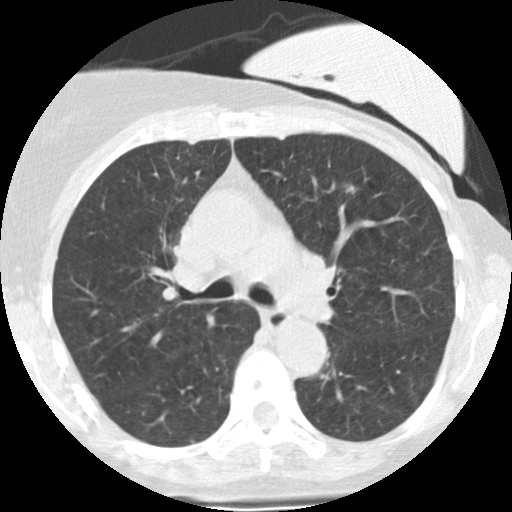
Chest CT (low-dose screening protocol), one axial image; second screening round (one year after baseline); lung window (W 1500 / L -600 HU); 2.5 mm slice thickness; slice 92 of 251 in the series. Female participant, aged 66 years at enrolment. Former smoker at enrolment.
• Expert reader's lesion annotation, box from (x=344, y=182) to (x=360, y=201) px.
• Reader record for this screening exam (exam-level; its link to the box is not recorded): non-calcified nodule or mass ≥4 mm, left upper lobe, 7 × 5 mm, smooth margins, soft tissue attenuation, pre-existing on the prior screen: yes; interval growth: yes.
• Participant outcome: lung cancer diagnosed 218 days after this screen — adenocarcinoma, NOS, left lower lobe, poorly differentiated (G3), stage IA (AJCC 6th edition), 8 mm at pathology.